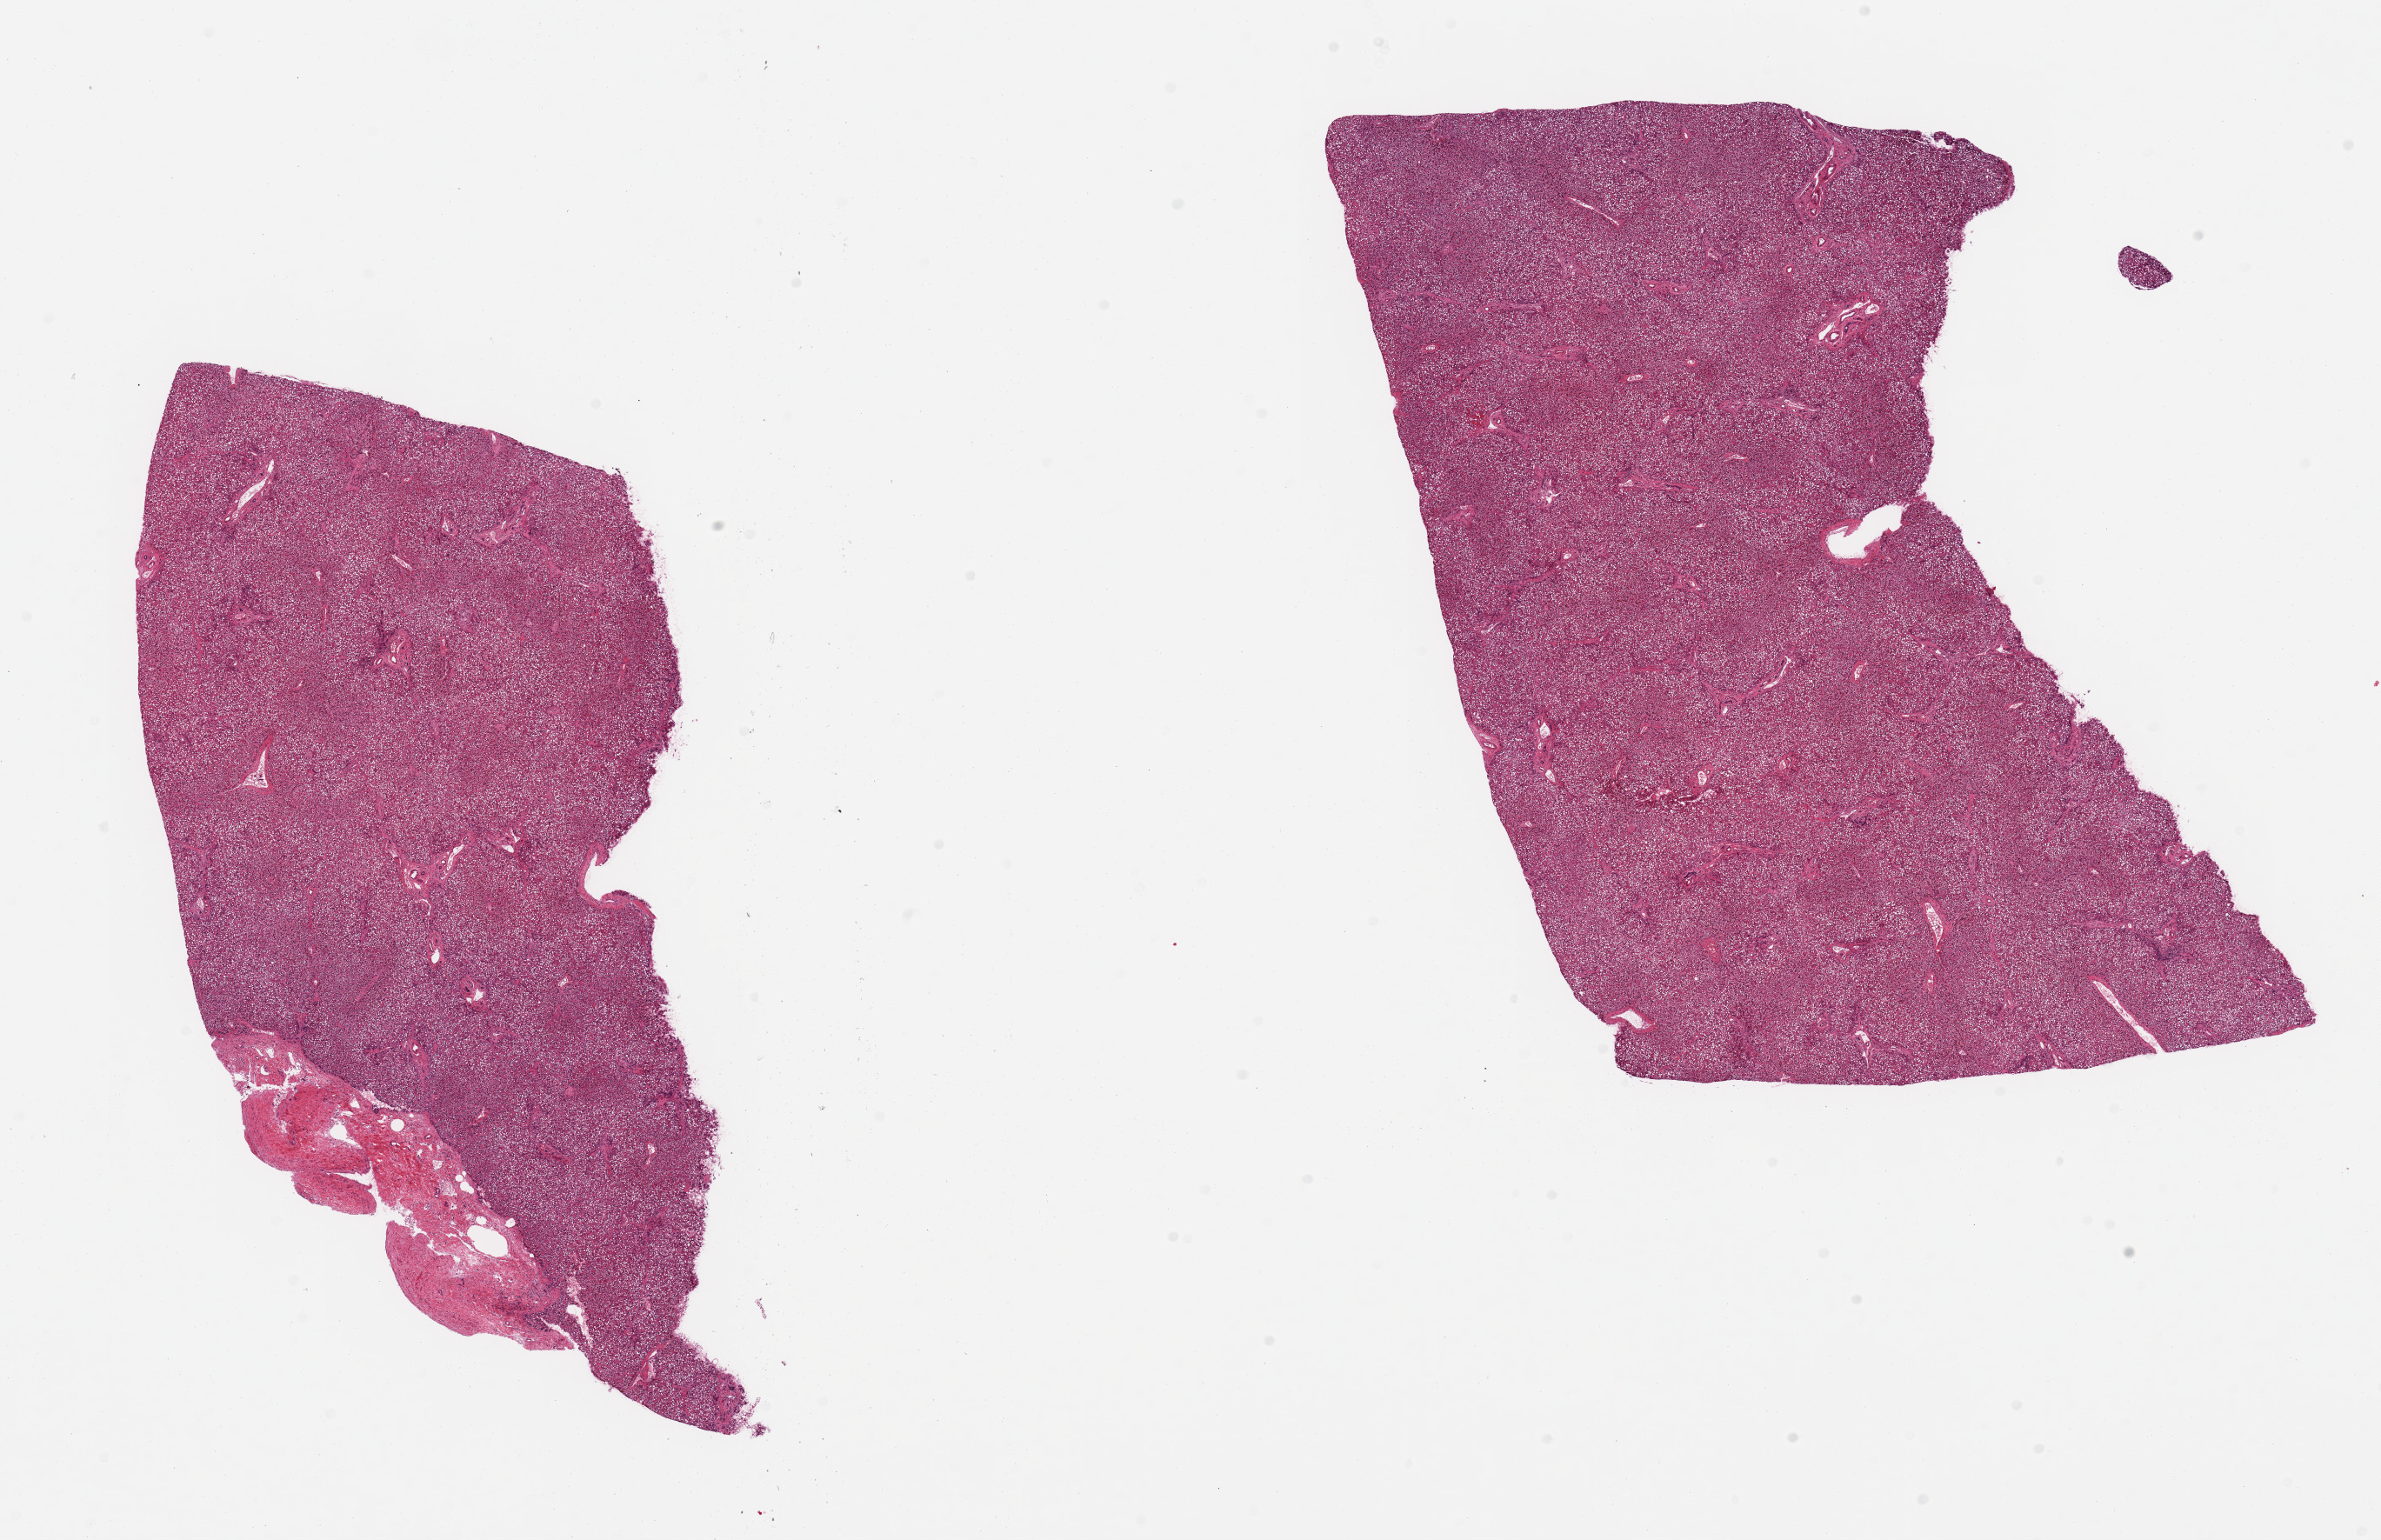
Whole-slide image, haematoxylin and eosin stain, brightfield — low-resolution overview of the scanned area, about 21.7 x 14.0 mm. PAXgene-fixed paraffin-embedded (PFPE) section. Section of liver (target tissue). Donor tissue sample. Donor sex: female.
Reviewer comment on this tissue sample: 2 pieces; extensive panlobular macrovesicular steatosis; fibrous tissue on edge of 1 piece occupies 20%.